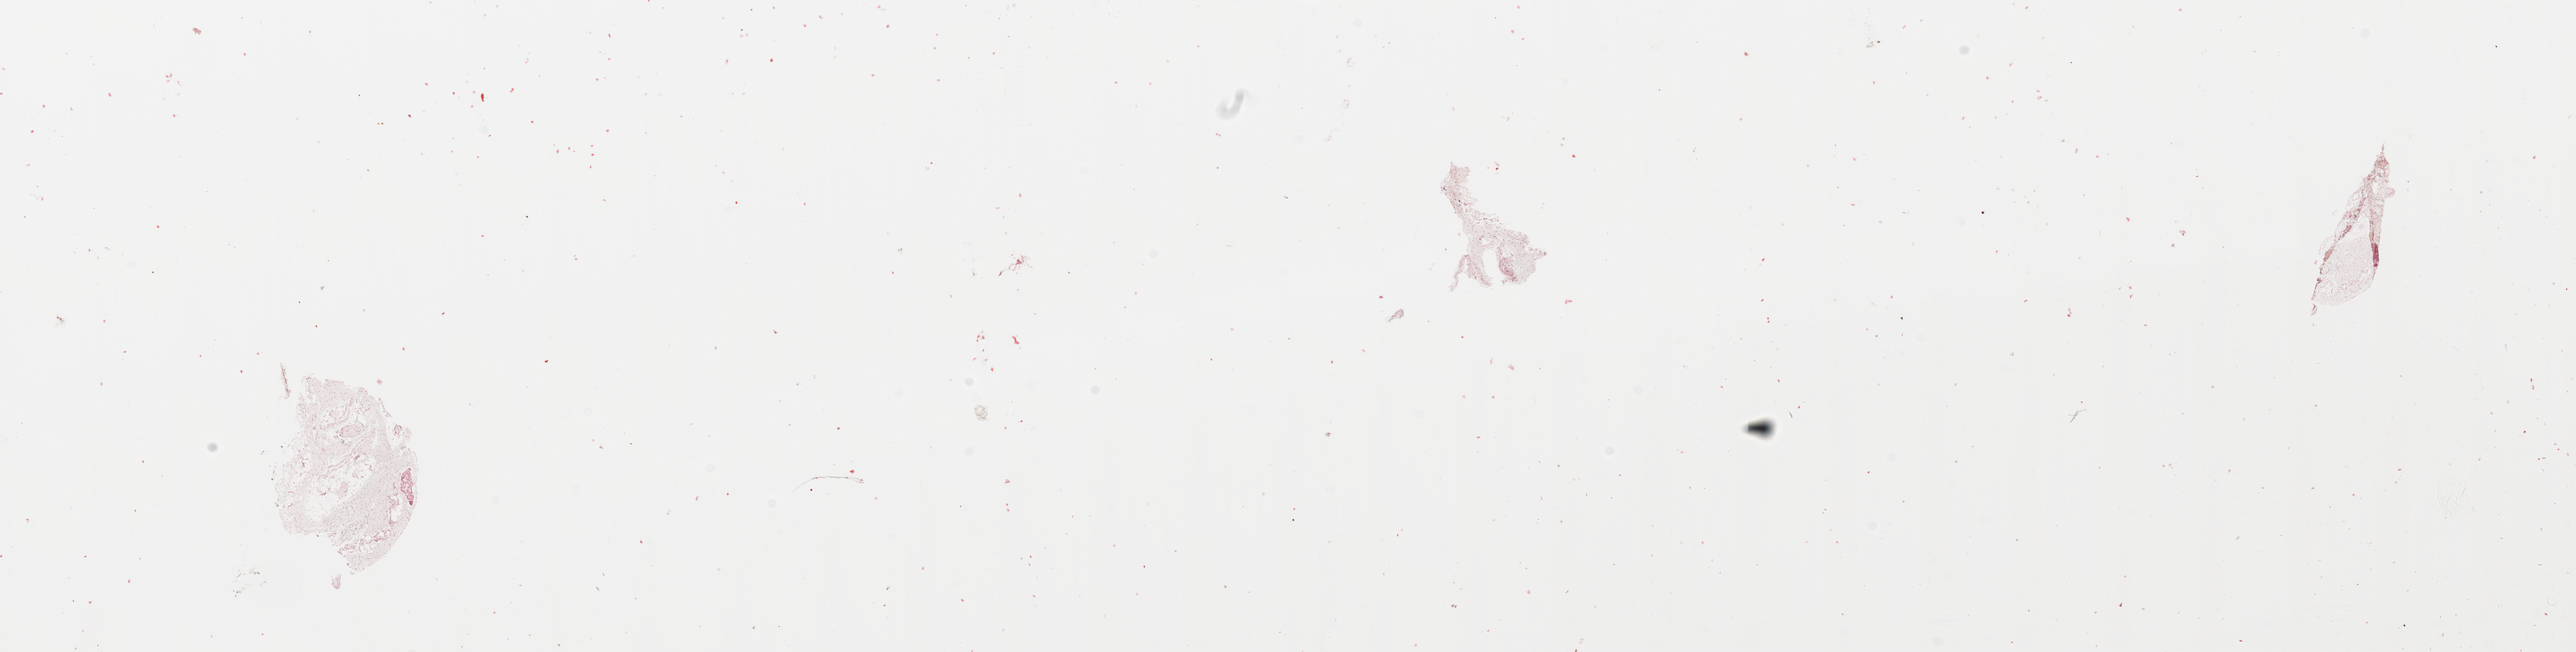
Digitized H&E-stained tissue section (whole slide), shown as a low-resolution overview of the whole scanned area (about 27.6 x 7.0 mm, acquisition: 20x scan); head and neck, tissue type not recorded. 61-year-old male patient.
Patient diagnosis: Squamous cell carcinoma, NOS (larynx, NOS).